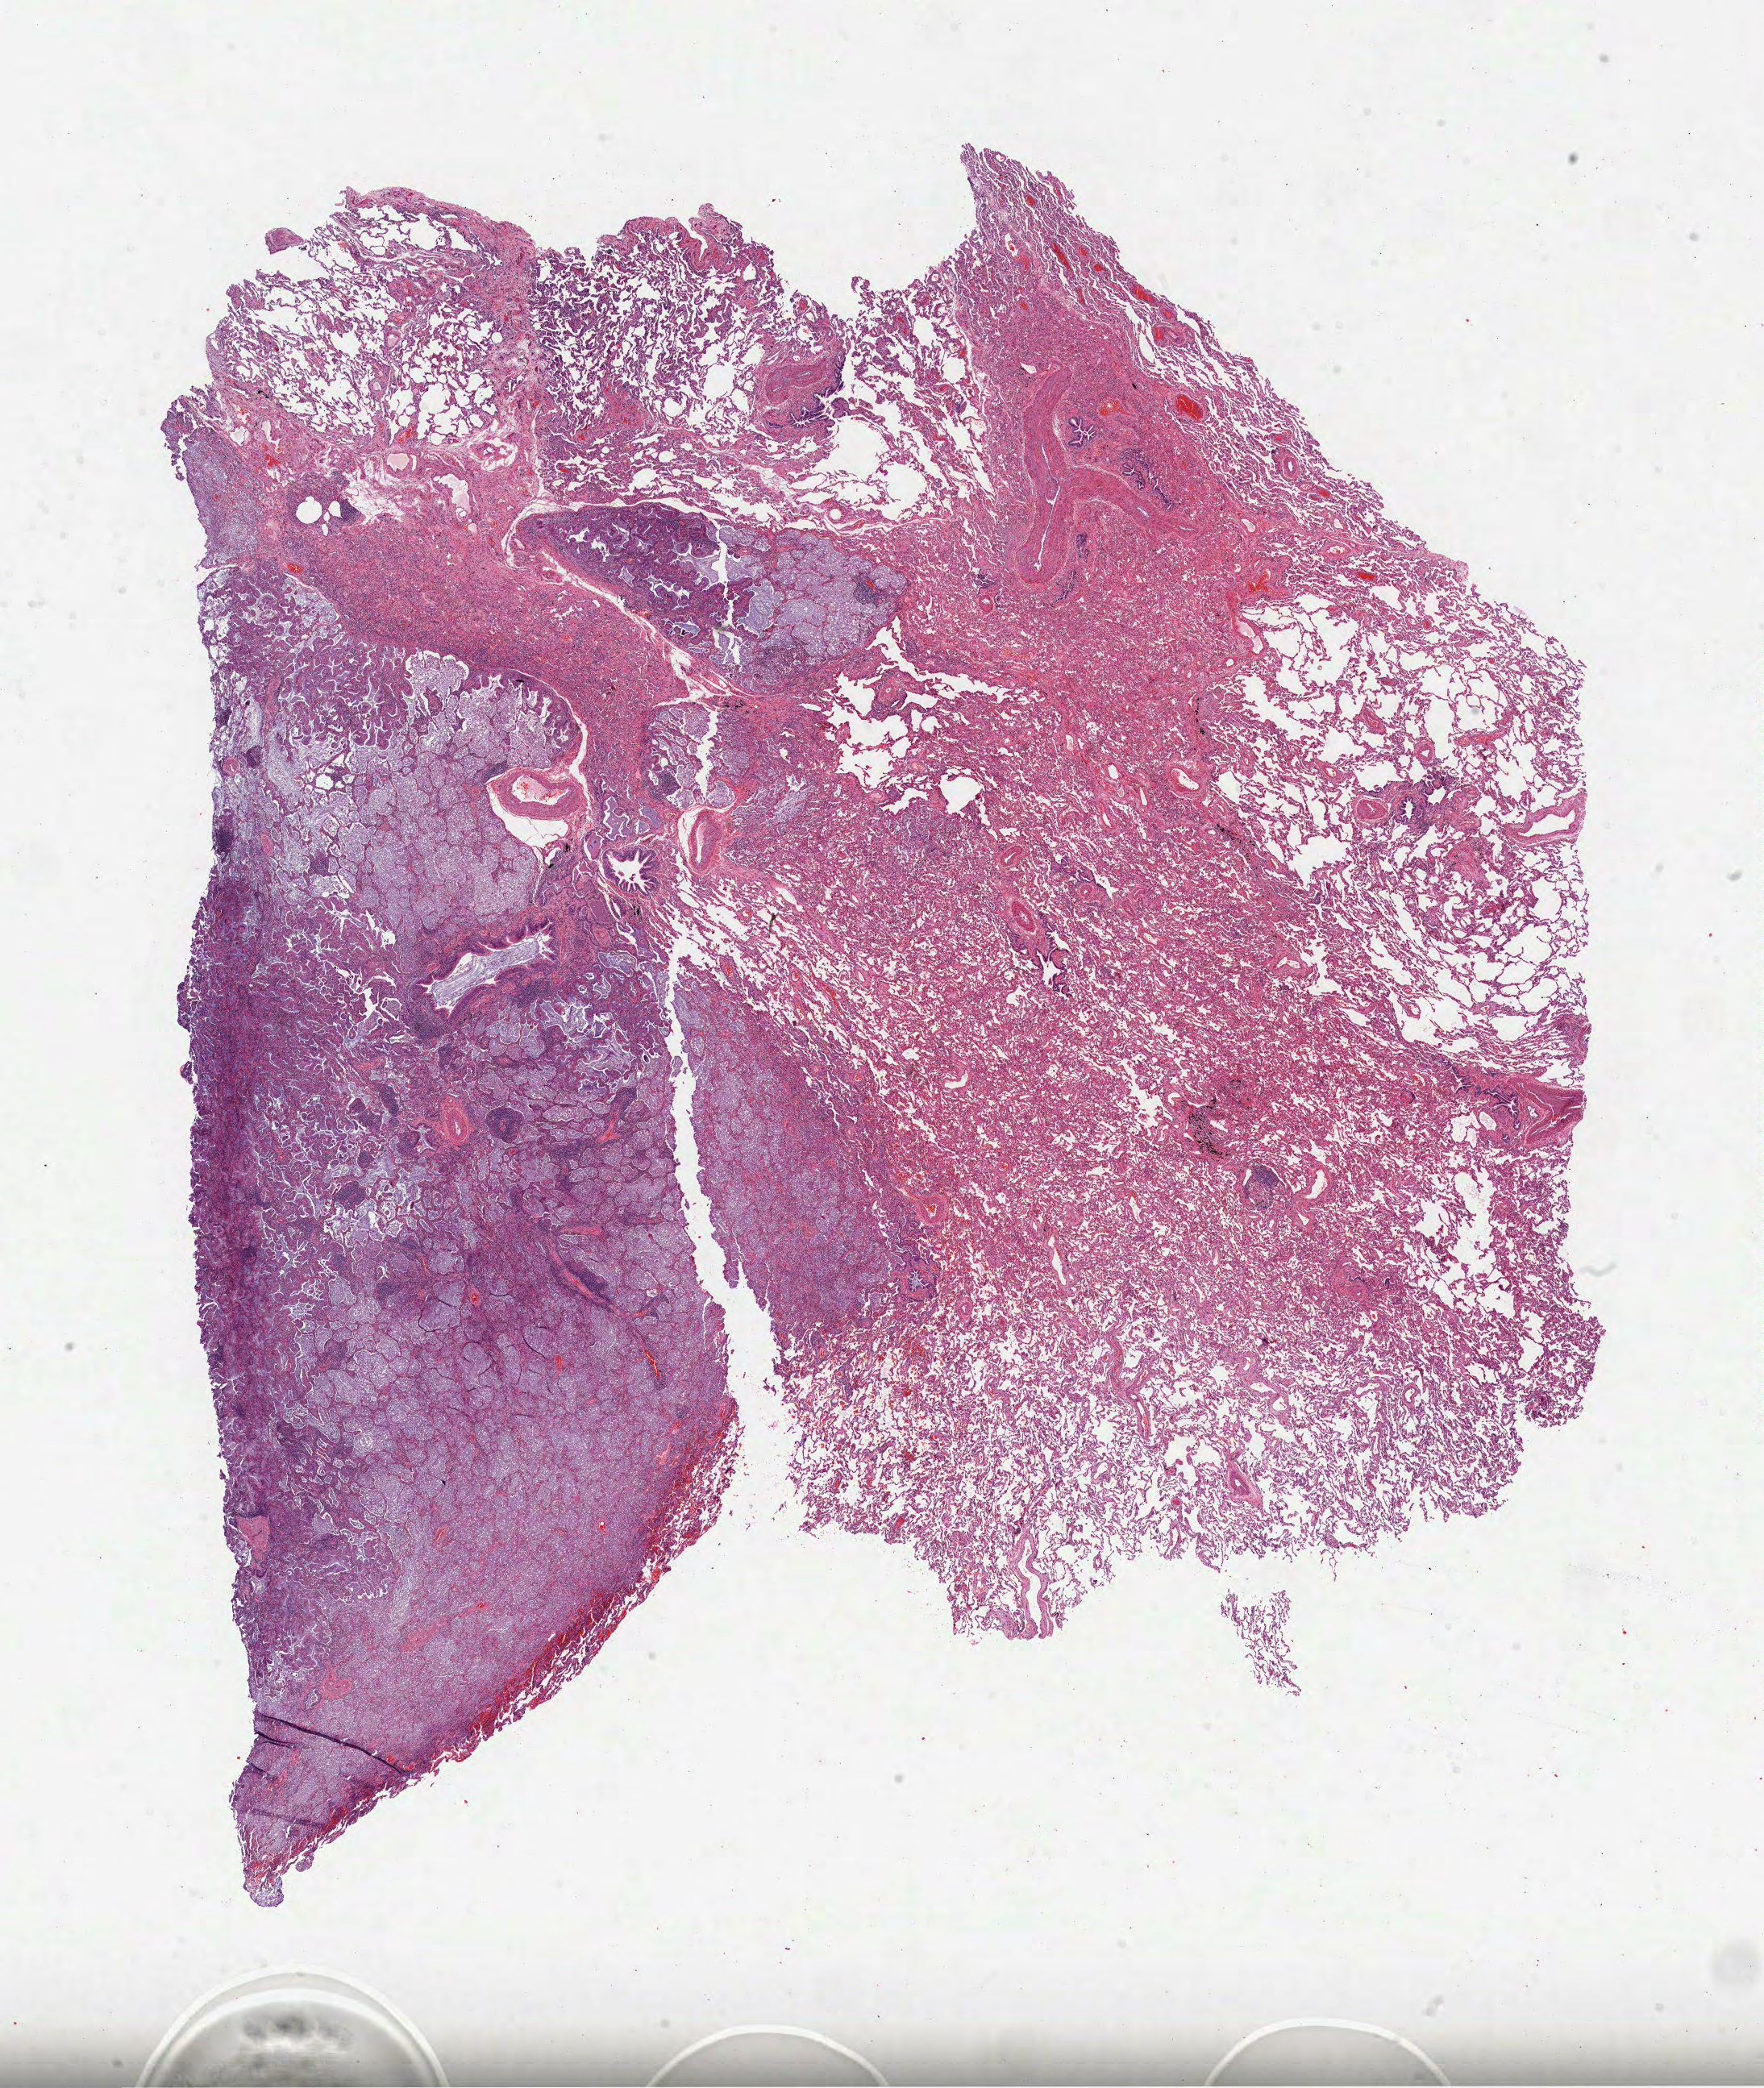
H&E-stained whole-slide image, shown as a low-resolution overview of the whole scanned area (about 17.6 x 20.9 mm, slide scanned at 40x). Formalin-fixed paraffin-embedded (FFPE) diagnostic section. Primary tumour sample from the lung. Male, age 70 years at initial diagnosis.
Laterality: left. AJCC pathologic stage: IB (6th edition). Diagnosis: Bronchio-alveolar carcinoma, mucinous (lower lobe, lung).